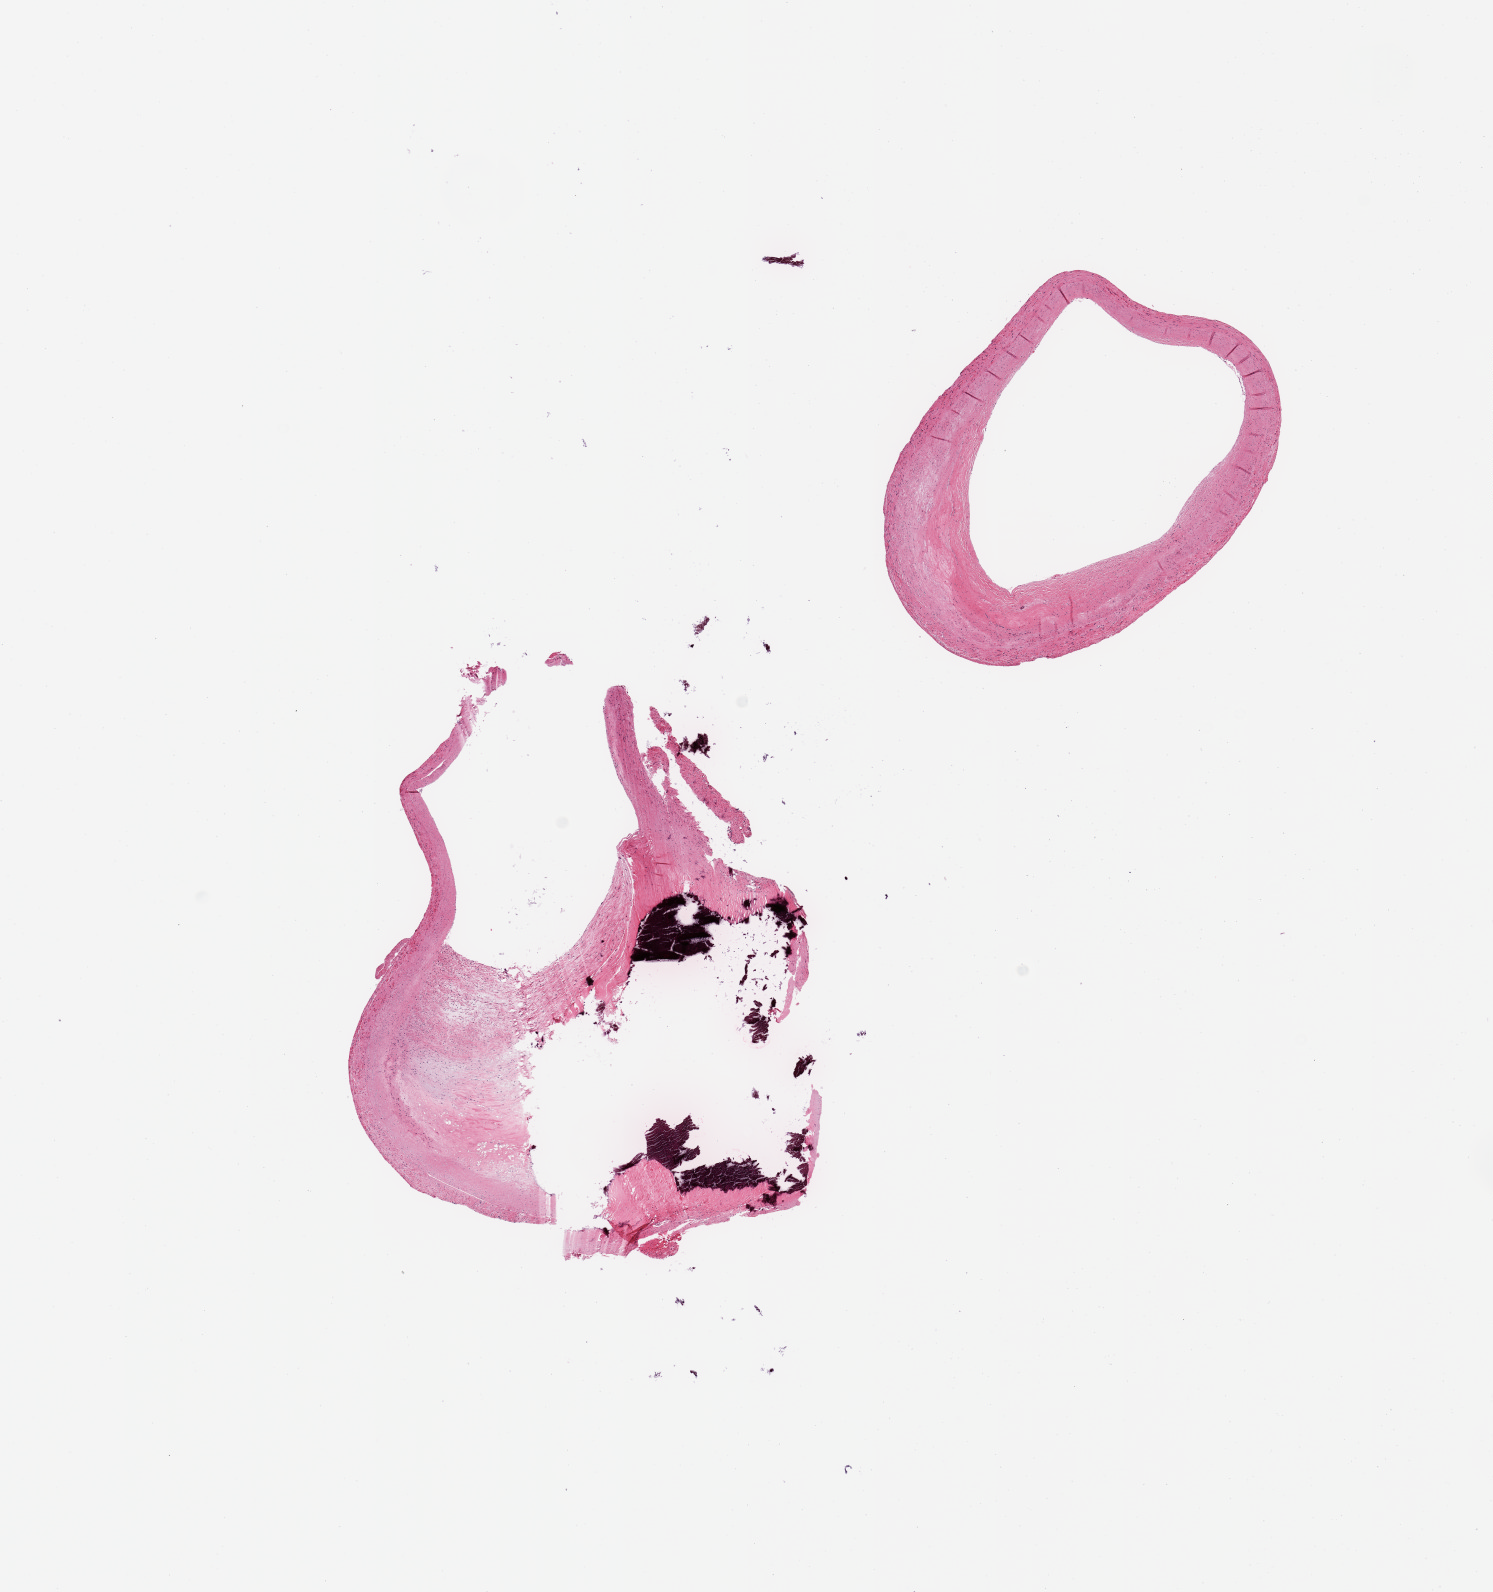
Digitized hematoxylin and eosin (H&E)-stained section — shown as a low-resolution overview of the whole scanned area (about 11.8 x 12.6 mm, acquisition: 20x scan). PAXgene-fixed paraffin-embedded (PFPE) section. Sampled site (target tissue): coronary artery. Donor tissue sample. Donor: male.
Review note (as recorded): 2 pieces; eccentric fibrosclerotic plaque and massive calcification narrowing lumen~50%.